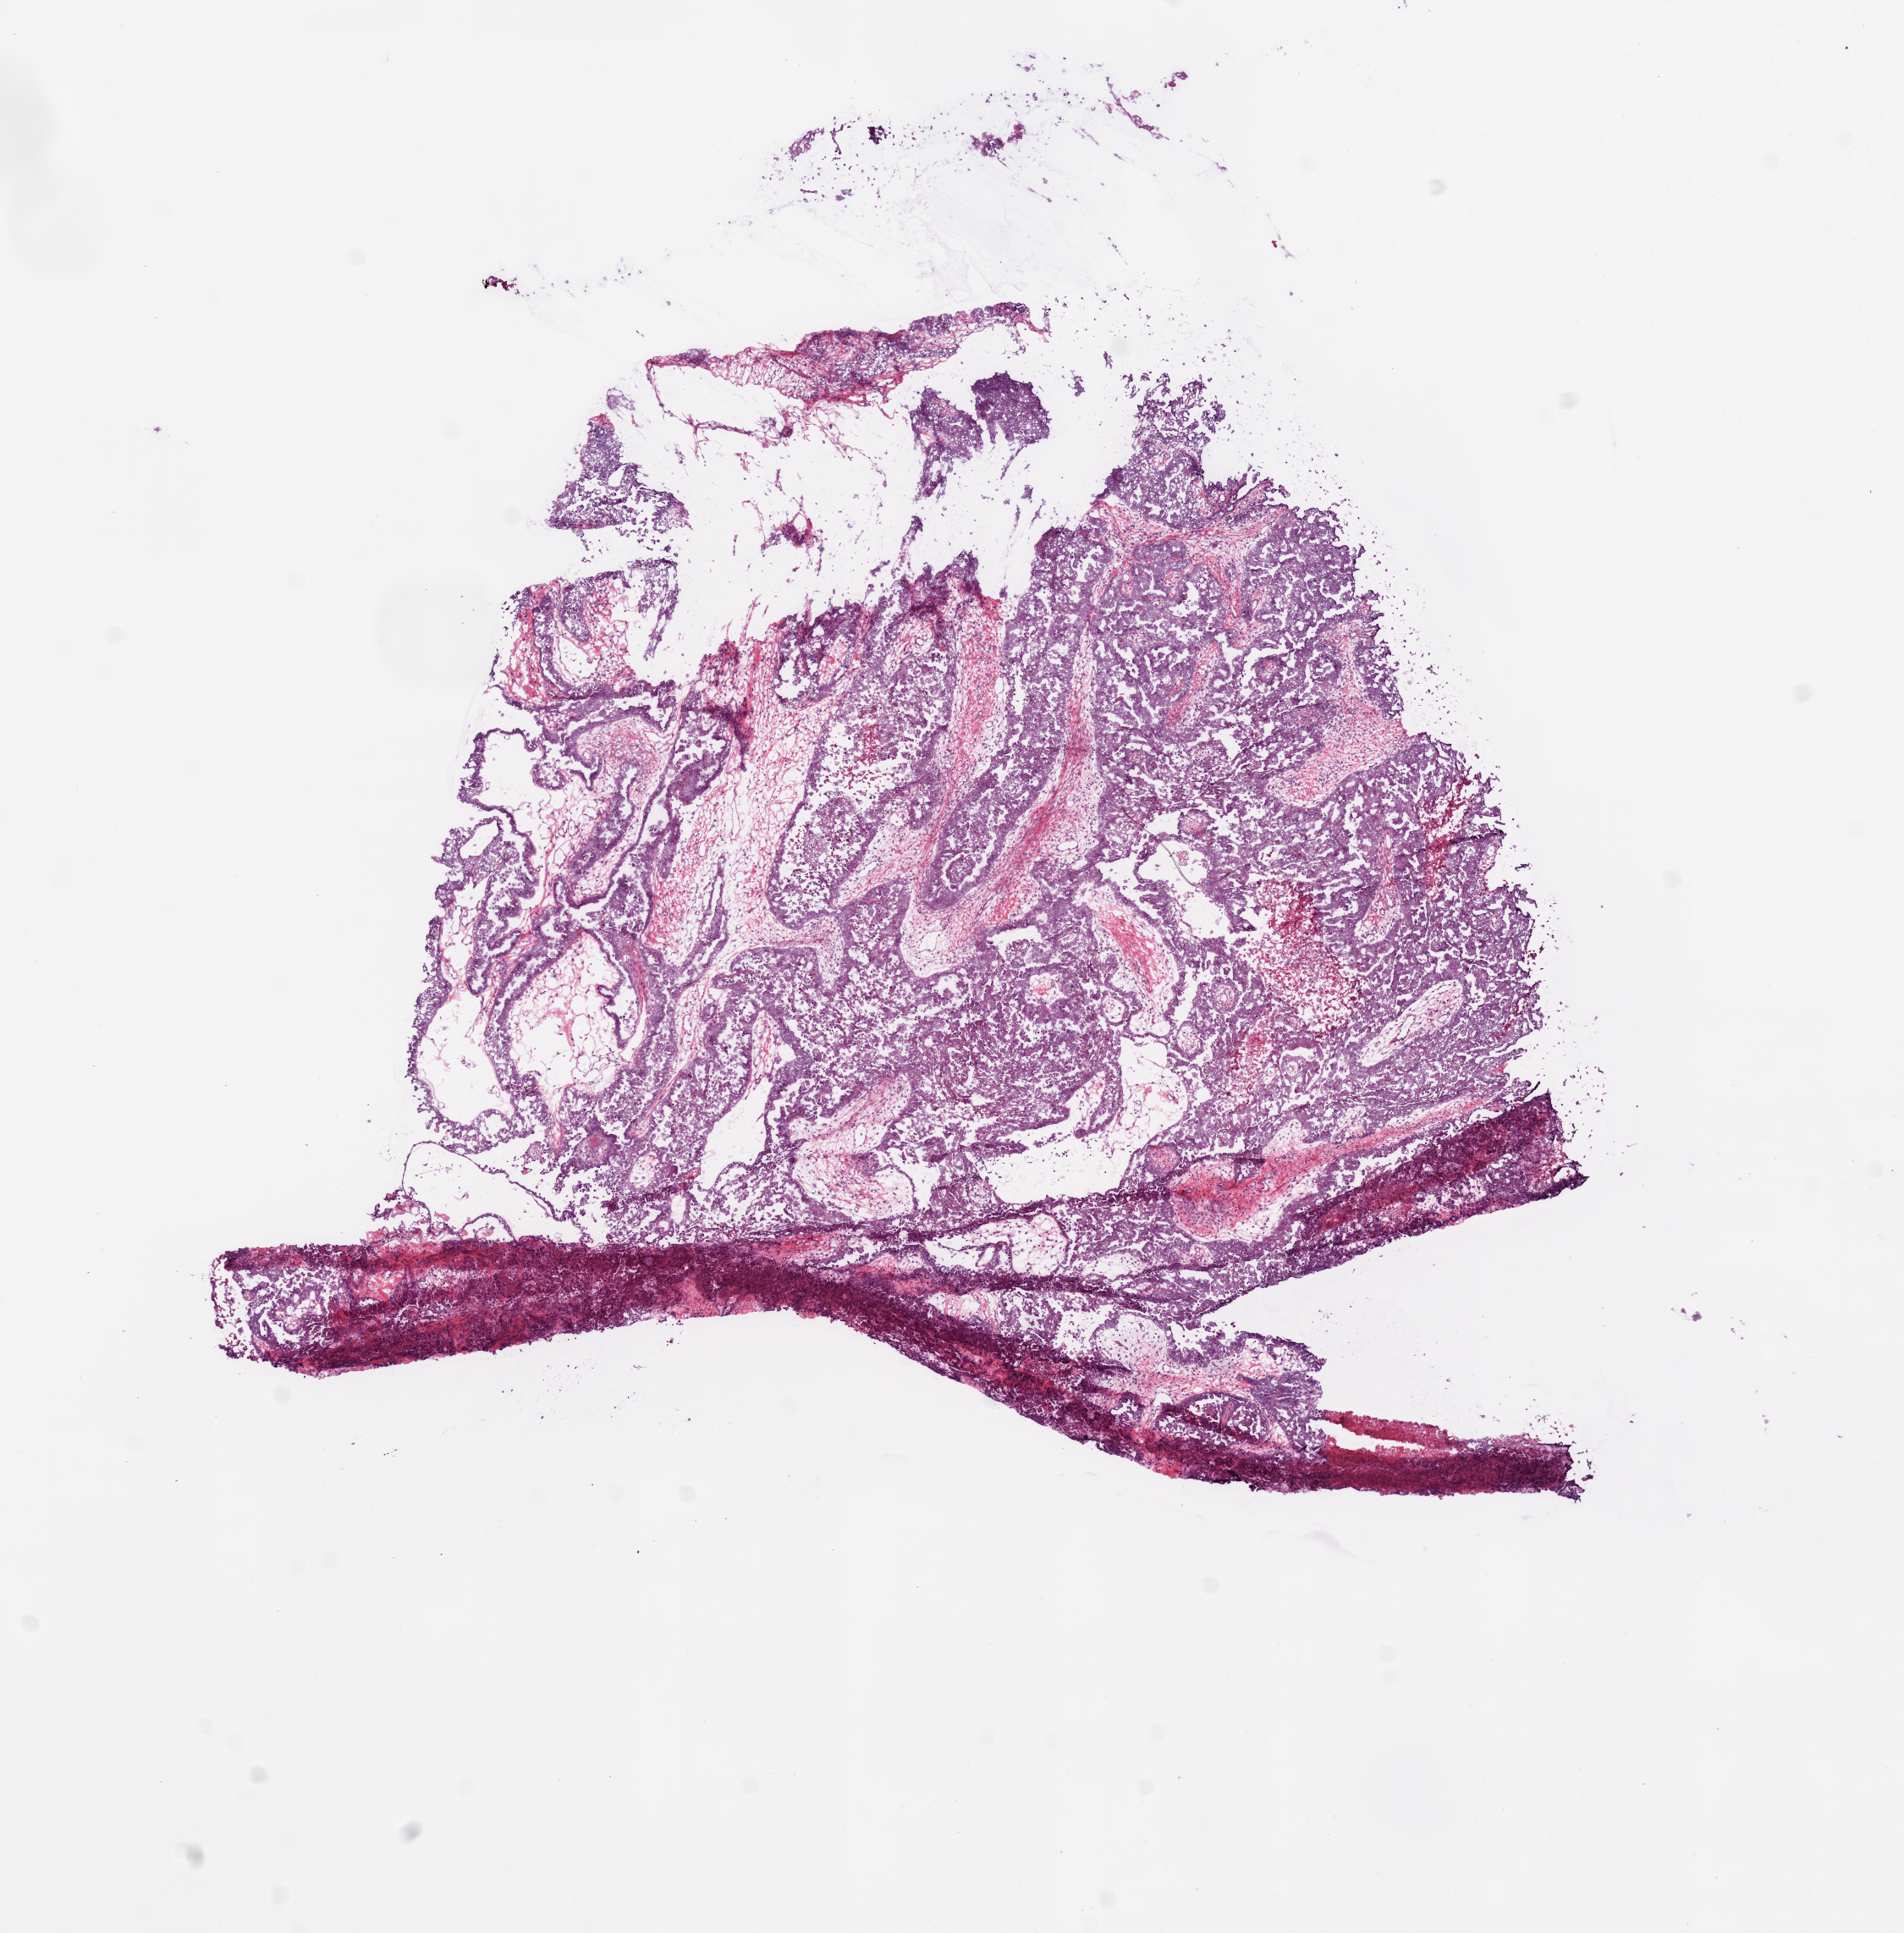
Whole-slide histology image, Hematoxylin and eosin (H&E) stained, shown as a low-resolution overview of the whole scanned area (about 9.0 x 9.2 mm, acquisition: 20x scan), frozen section, primary tumour sample from the ovary. Patient: female, age at initial diagnosis 74 years. Histologic grade: G3 (poorly differentiated). Slide review estimates, as recorded: tumour cells 70%, tumour nuclei 80%, normal cells 0%, stromal cells 30%, necrosis 0%.
FIGO stage: IIIC. Diagnosis: Serous cystadenocarcinoma, NOS.